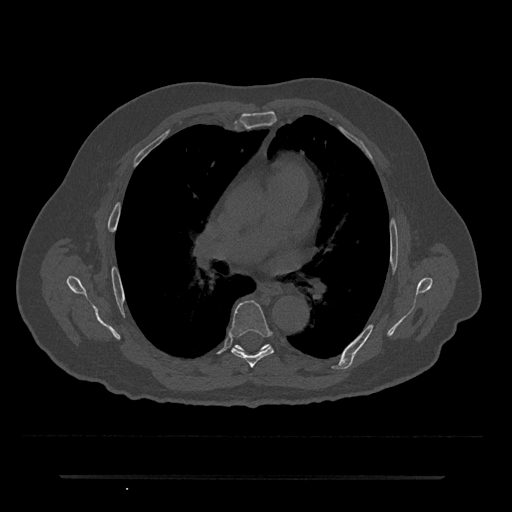
CT including the spine, one axial slice. Slice 426 of 797 in the series (ordered by position). Reconstruction kernel Br40s/3. 120 kVp. Bone window (W 1800 / L 400 HU). 0.5 mm slice thickness. 512 × 512 image matrix. Patient: male, 69 years. Case-level facts recorded for this patient, not image findings: primary cancer: prostate.
Outlined on this slice (semi-automatic segmentation, software-assisted and operator-edited):
- T6 vertebra: bounding box (x1, y1, x2, y2) in pixels: (229, 301, 274, 368)
- T7 vertebra: (236, 346, 241, 349)